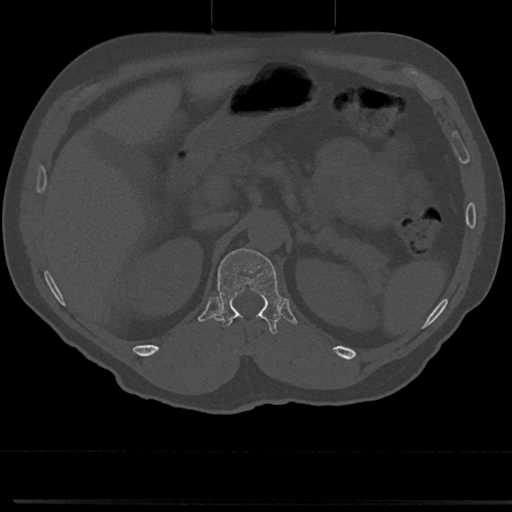
CT including the spine, one axial slice. Position 149 of 817 along the scan axis. Reconstruction kernel Br40s/3. 120 kVp. Bone window (W 1800 / L 400 HU). 0.5 mm slice thickness. 512 × 512 image matrix, field of view 355 × 355 mm. Patient: male, 61 years. Case-level facts recorded for this patient, not image findings: primary cancer: prostate.
Annotated regions visible in this slice (semi-automatically segmented with operator editing):
- T12 vertebra: bounding box <213,245,279,335> (left, top, right, bottom; pixels)